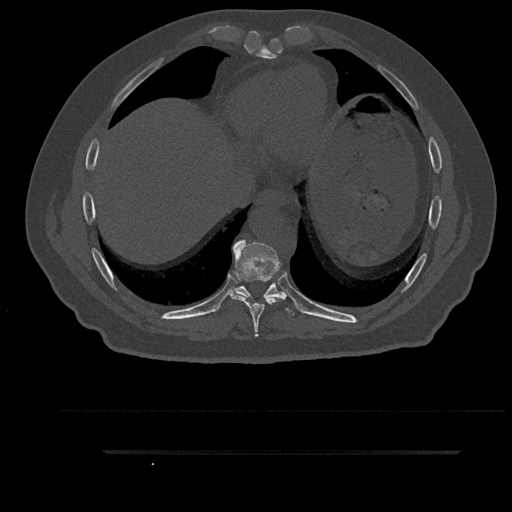
CT including the spine, one axial slice. Slice 451 of 797 in the series (ordered by position). Reconstruction kernel Br40s/3. 120 kVp. Bone window (W 1800 / L 400 HU). 0.5 mm slice thickness. 512 × 512 image matrix. Male patient, age 63 years. Case-level facts recorded for this patient, not image findings: primary cancer: renal; vertebrae with lytic lesions (as recorded): T8.
Outlined on this slice (semi-automatically segmented with operator editing):
- T8 vertebra: box from (x=229, y=239) to (x=286, y=337) px
- T9 vertebra: (x=231, y=252)–(x=295, y=316)